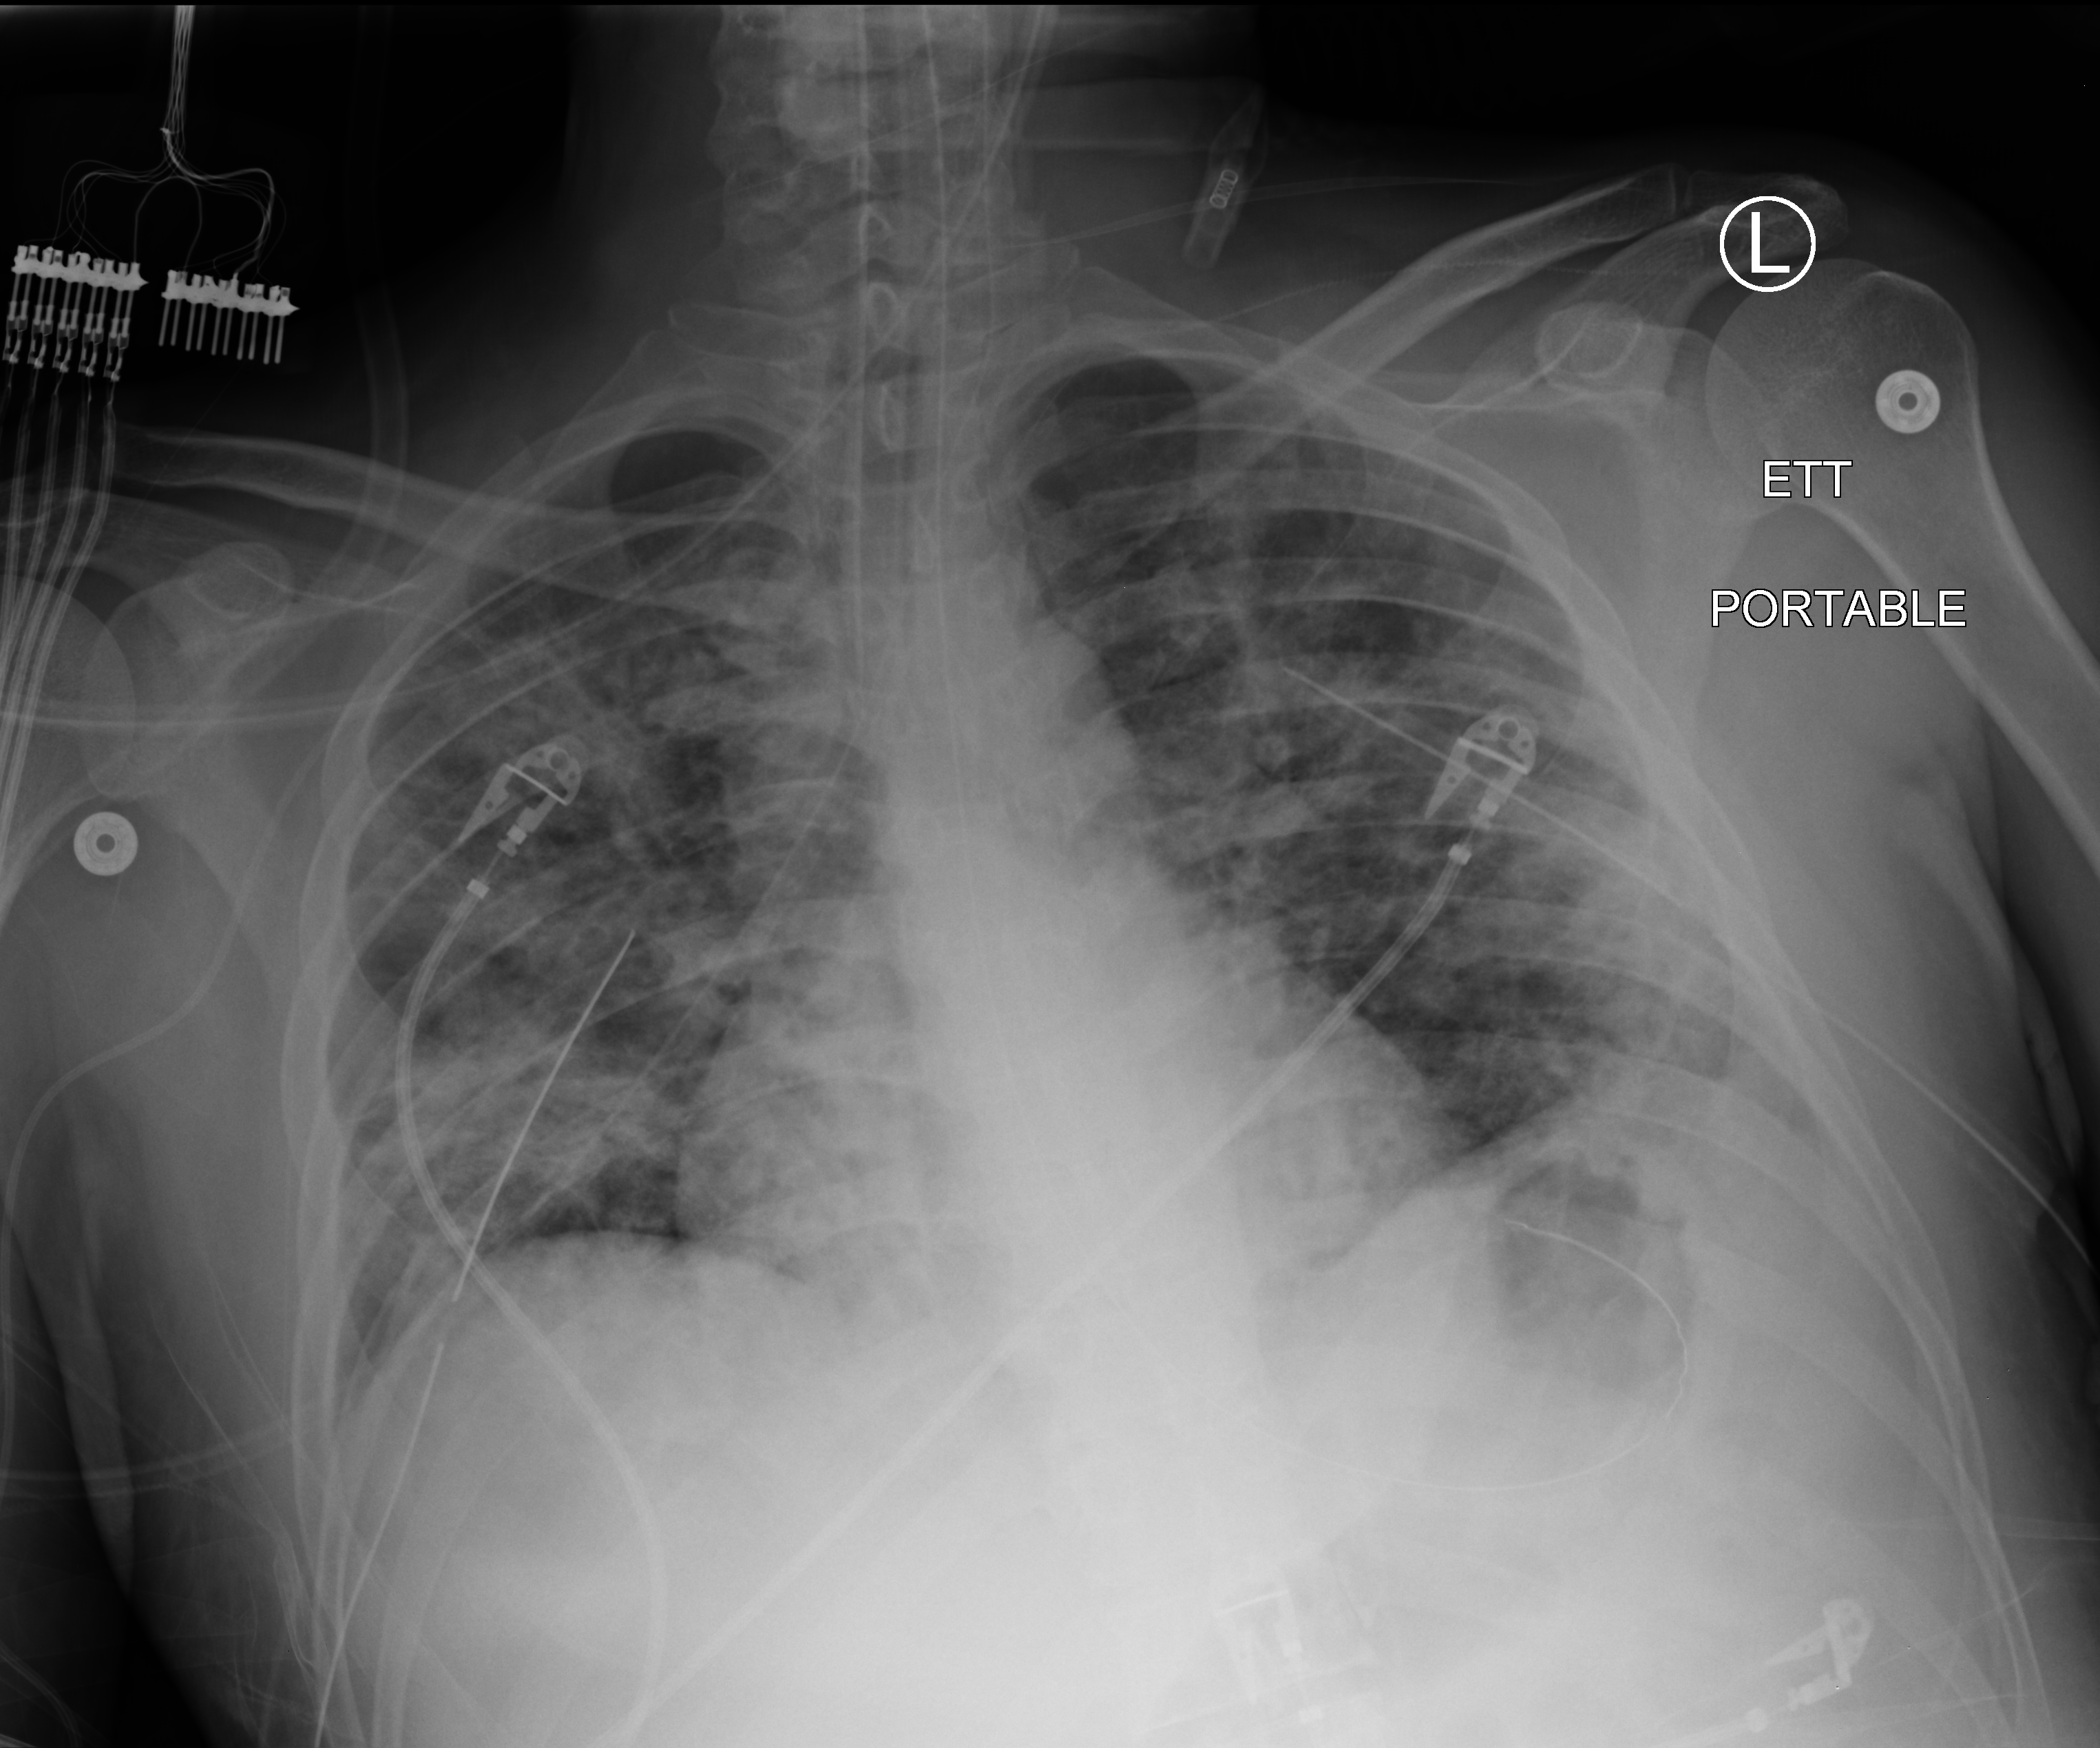
Portable chest radiograph, anteroposterior (AP) projection. Patient hospitalised with COVID-19; male, aged 18–59 years.
Hospital-stay facts (about this admission, not read from this image; timing relative to this image not recorded): admitted to intensive care during this hospital stay: yes; mechanically ventilated during this hospital stay: yes; smoking status (admission record): never.